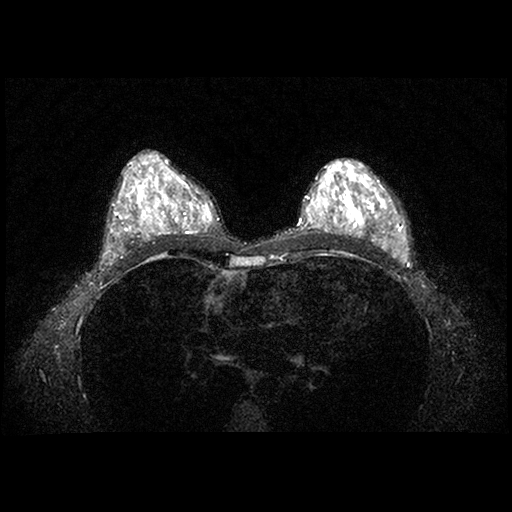
Breast MRI examination; 2 images, each one mid-volume slice chosen by position.
Image 1: axial T2-weighted / STIR image, series "STIR SENSE", slice 43 of 84.
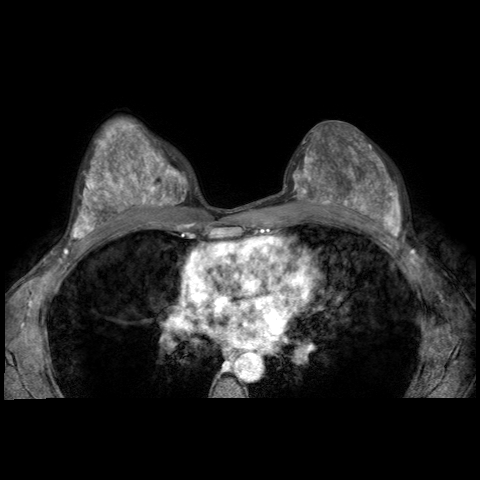
Image 2: post-contrast dynamic axial slice, series "AX BLISS_AUTO SENSE", slice 32 of 62, dynamic phase 5 of 8.
Radiologist's MRI impression, right breast: Post lumpectomy changes in the right breast. Residual cluster of indeterminate calcifications in the upper-outer quadrant of the right breast.
Patient-level pathology facts (from the clinical record, not from the images): pathology diagnosis: ductal CA in situ (right breast); receptor status (as recorded): ER pos, PR pos, HER2 pos; pathology report notes: post surg path [date] showed only scar.